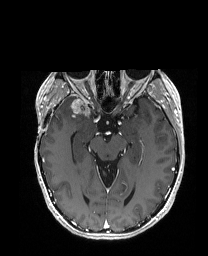
Brain MRI from a brain-tumour surgery series, one axial slice. Position 108 of 192 along the scan axis. T1-weighted post-contrast. 1 mm slice thickness. 208 × 256 image matrix, field of view 203 × 250 mm. Case-level facts recorded for this patient, not image findings: histopathology: Metastatic Carcinoma from Breast primary.
Structures marked on this image (outlined manually by an expert reader):
- tumour: bounding box <68,97,88,114> (left, top, right, bottom; pixels)